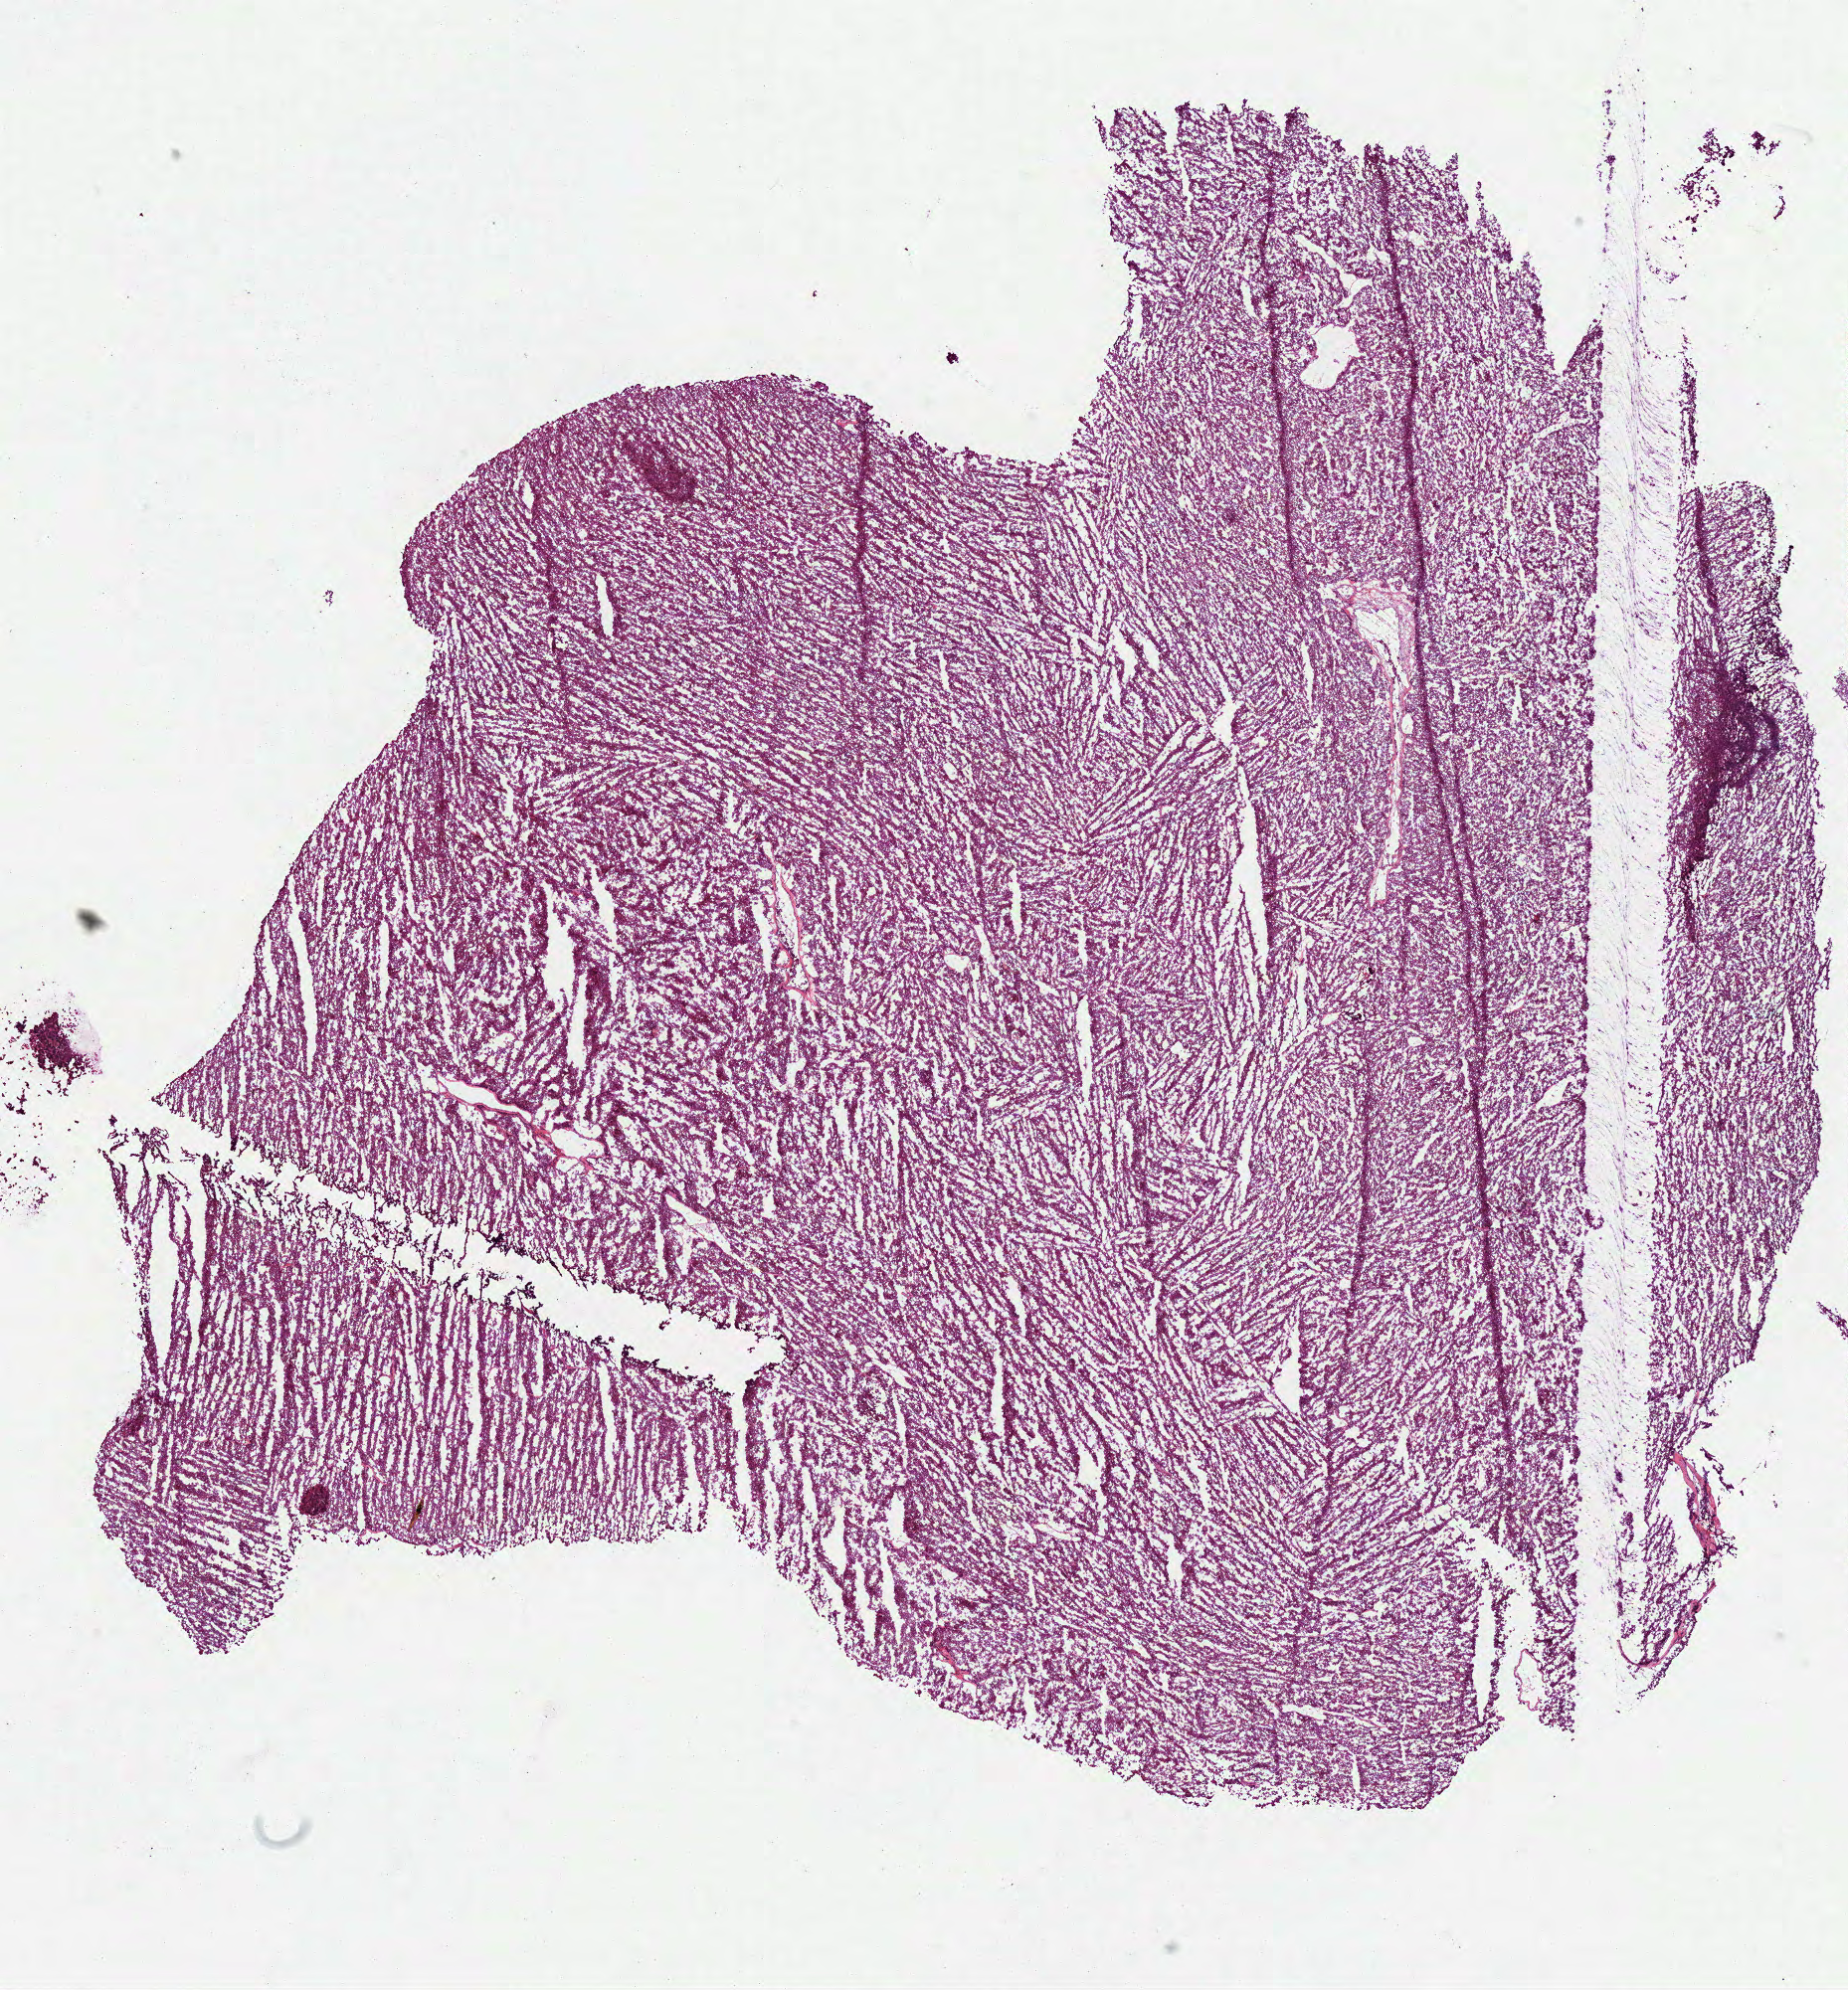
Digitized H&E tissue section (whole slide) — low-resolution overview of the scanned area, about 15.0 x 16.1 mm (slide scanned at 40x). Frozen section from the bottom of the tissue portion. Primary tumour sample from the kidney. Male patient; age at initial diagnosis 62 years. Pathologist review of this section (percent, as recorded): tumour cells 100%, tumour nuclei 95%, normal cells 0%, stromal cells 0%, necrosis 0%. Inflammatory infiltration, as recorded: lymphocyte infiltration 0%, monocyte infiltration 0%, neutrophil infiltration 0%.
Histologic diagnosis: Renal cell carcinoma, chromophobe type. AJCC pathologic stage: II (6th edition).